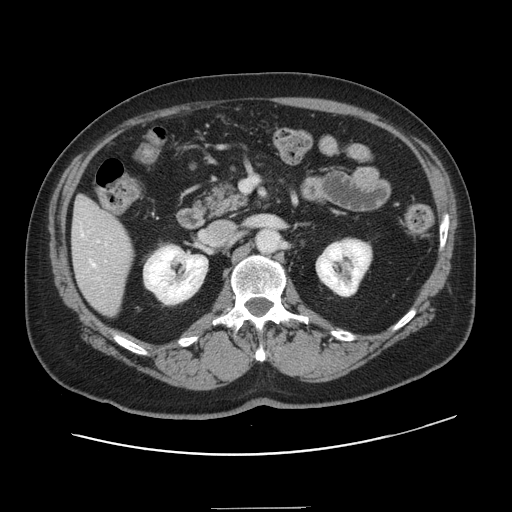
Contrast-enhanced abdominal CT, one axial slice; intravenous contrast given; soft-tissue window (W 400 / L 40 HU); 2.5 mm slice thickness; 512 × 512 image matrix, field of view 402 × 402 mm. Male patient, age 62 years. From the clinical record (not read from this slice): diagnosis: colorectal cancer liver metastases, imaged before liver resection; multiple liver metastases: yes; largest metastasis: 2.7 cm.
Structures marked on this image (expert manual segmentation):
- hepatic veins: bounding box [x1, y1, x2, y2] px = [81, 233, 96, 267]
- liver: [73, 198, 133, 316]
- planned liver remnant (the part of the liver to remain after resection): [79, 198, 90, 207]
- portal vein (with intrahepatic branches): [97, 240, 107, 262]